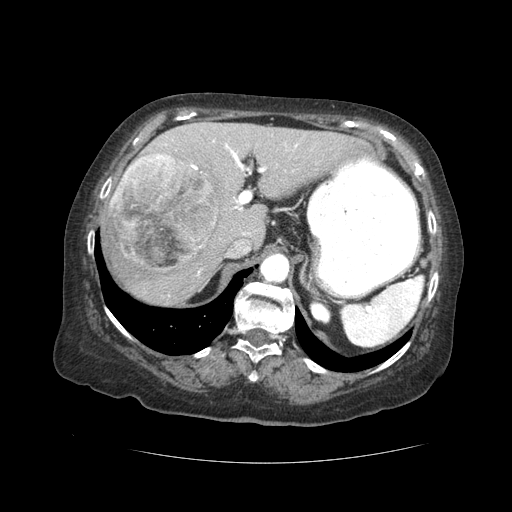
Contrast-enhanced abdominal CT (liver protocol), one axial slice. Reconstruction kernel STANDARD. 120 kVp. Soft-tissue window (W 400 / L 40 HU). 2.5 mm slice thickness. 512 × 512 image matrix, field of view 380 × 380 mm. Case-level facts recorded for this patient, not image findings: diagnosis: hepatocellular carcinoma (patient treated with transarterial chemoembolisation; whether this scan precedes or follows treatment is not stated here); TNM stage (as recorded): Stage-I; Child-Pugh class: A; tumour nodularity: uninodular.
Annotated regions visible in this slice (semi-automatic segmentation, software-assisted and operator-edited):
- liver parenchyma outside the tumour (the mass and vessels are separate outlines, so this box may not span the whole liver): box from (x=102, y=122) to (x=362, y=304) px
- mass: (x=110, y=154)–(x=219, y=272)
- liver vessels: (x=164, y=140)–(x=299, y=274)